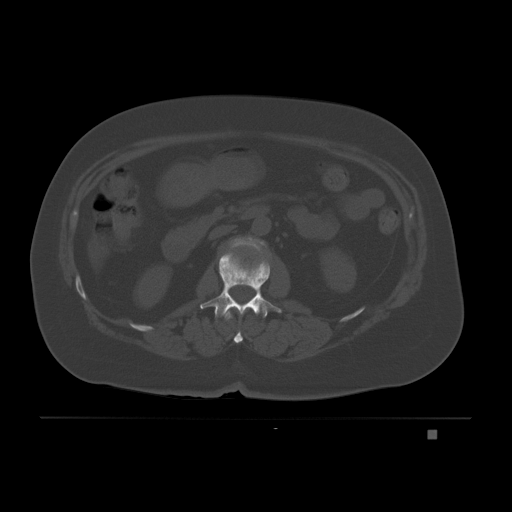
CT including the spine, one axial slice. Slice 70 of 221 in the series (ordered by position). Bone window (W 1800 / L 400 HU). 3 mm slice thickness. 512 × 512 image matrix. Female patient, age 63 years. From the clinical record (not read from this slice): primary cancer: breast.
Structures marked on this image (semi-automatically segmented with operator editing):
- L1 vertebra: bounding box (x1, y1, x2, y2) in pixels: (200, 251, 282, 320)
- L2 vertebra: (230, 237, 265, 252)
- T12 vertebra: (231, 316, 243, 343)